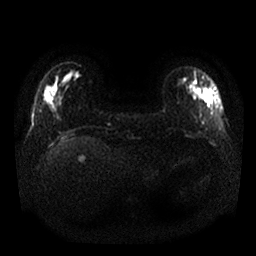
Breast MRI, one axial slice. Position 4 of 25 along the scan axis. Diffusion-weighted series; image 2 of 4 stored at this slice position (different b-values; order by instance number). 1.5 T. 4 mm slice thickness. 256 × 256 image matrix, field of view 340 × 340 mm. Female patient.
Structures marked on this image (outlined manually by an expert reader):
- tumour on diffusion-weighted imaging: bounding box (x1, y1, x2, y2) in pixels: (200, 86, 214, 108)